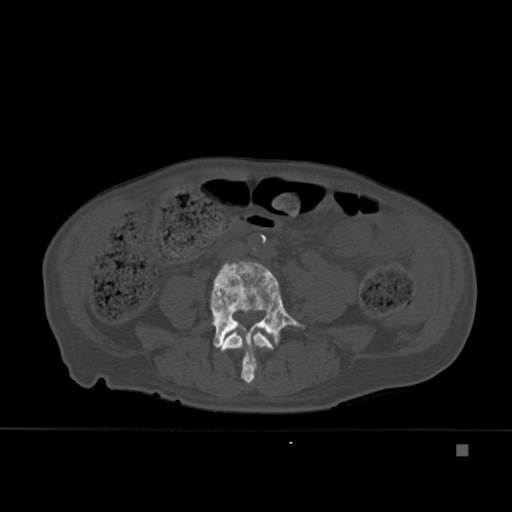
CT including the spine, one axial slice; slice 128 of 451 in the series (ordered by position); bone window (W 1800 / L 400 HU); 1.5 mm slice thickness; 512 × 512 image matrix, field of view 378 × 378 mm. Male patient, age 75 years. From the clinical record (not read from this slice): primary cancer: prostate.
Annotated regions visible in this slice (semi-automatic segmentation, software-assisted and operator-edited):
- L3 vertebra: bounding box (x1, y1, x2, y2) in pixels: (221, 331, 274, 384)
- L4 vertebra: (210, 261, 305, 383)